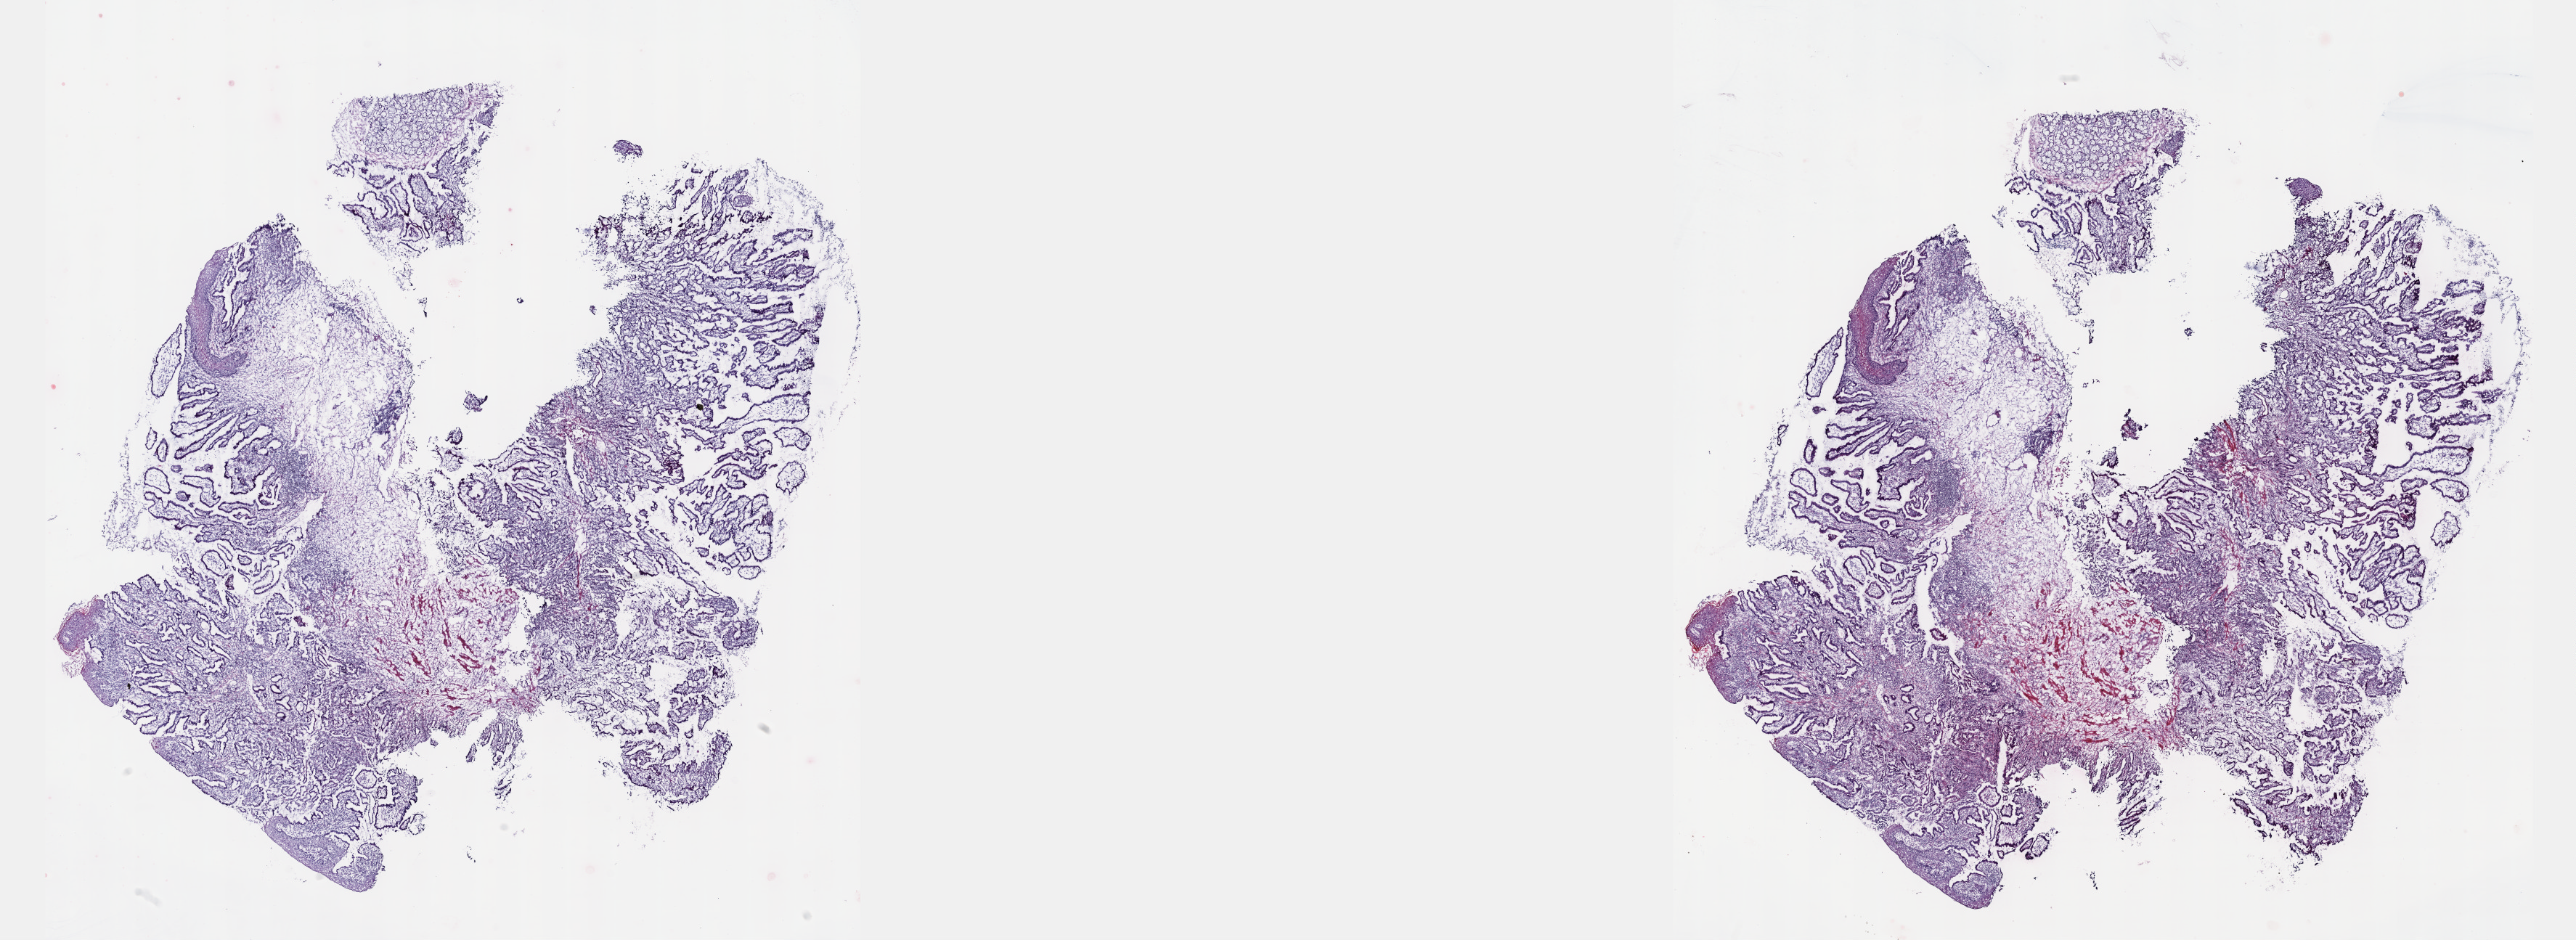
Digitized H&E tissue section (whole slide) — low-resolution overview of the scanned area, about 28.7 x 10.5 mm (slide scanned at 40x), frozen section from the top of the tissue portion, stomach, primary tumour sample. Male, age 63 years at initial diagnosis. Histologic grade: G2 (moderately differentiated). Slide review estimates, as recorded: tumour cells 95%, tumour nuclei 65%, normal cells 5%, stromal cells 0%, necrosis 0%. Inflammatory infiltration, as recorded: lymphocyte infiltration 7%, monocyte infiltration 0%, neutrophil infiltration 0%.
- lymph nodes positive (case pathology): 0 of 39 examined
- AJCC pathologic stage: IA (7th edition)
- histologic diagnosis: Adenocarcinoma, NOS